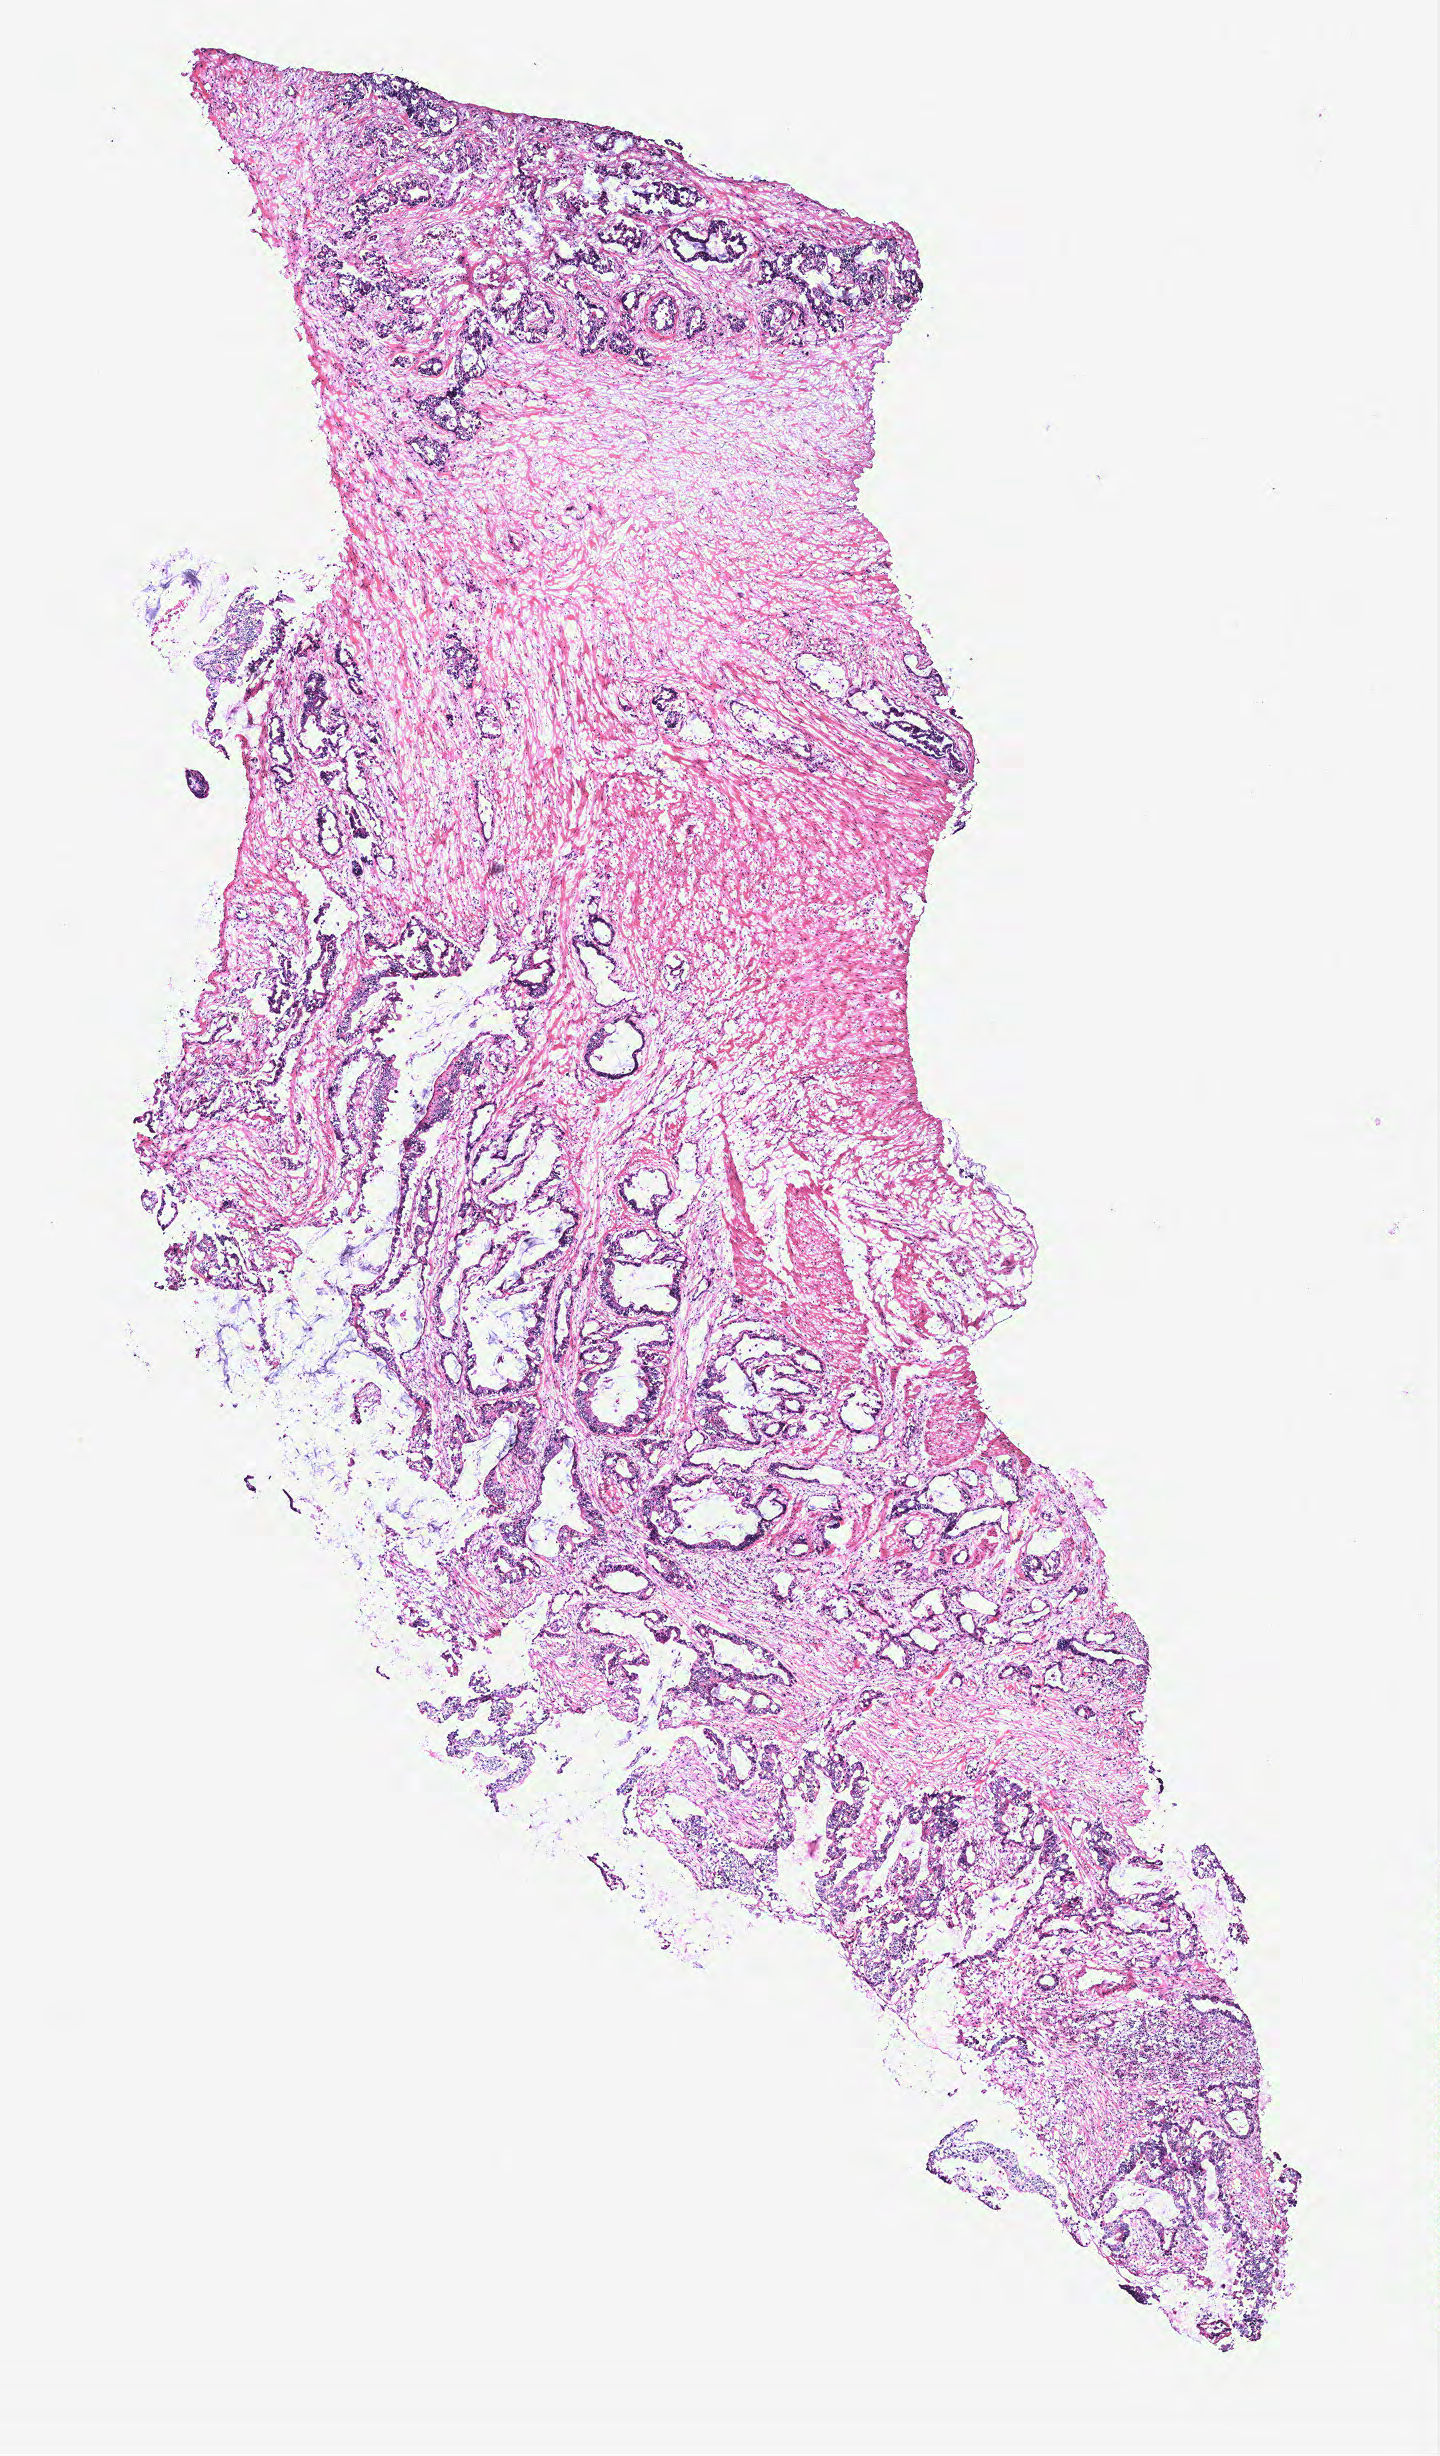
Whole-slide histology image, H&E-stained — low-resolution overview of the scanned area, about 5.8 x 9.8 mm (from a 40x scan). Colon, tissue type not recorded.
* patient diagnosis (cohort enrolment): colon cancer (colon)